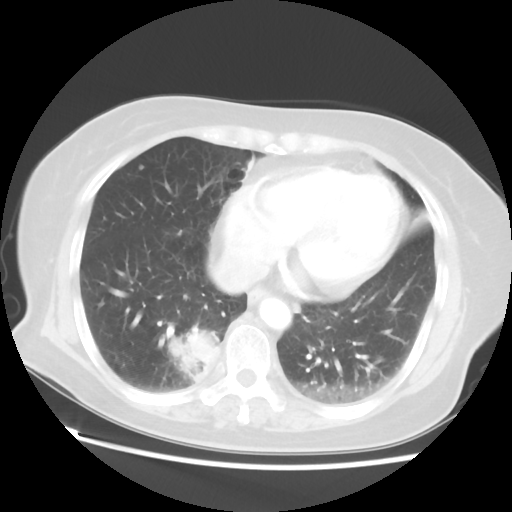
Chest CT, one axial slice; 120 kVp; lung window (W 1500 / L -600 HU); 5 mm slice thickness; 512 × 512 image matrix, field of view 356 × 356 mm. Female patient, age 69 years. Case-level facts recorded for this patient, not image findings: clinical TNM (as recorded): T2 N1 M1a.
Annotated regions visible in this slice (bounding box drawn by a radiologist):
- lung tumour (recorded histology: adenocarcinoma): box from (x=167, y=324) to (x=225, y=388) px